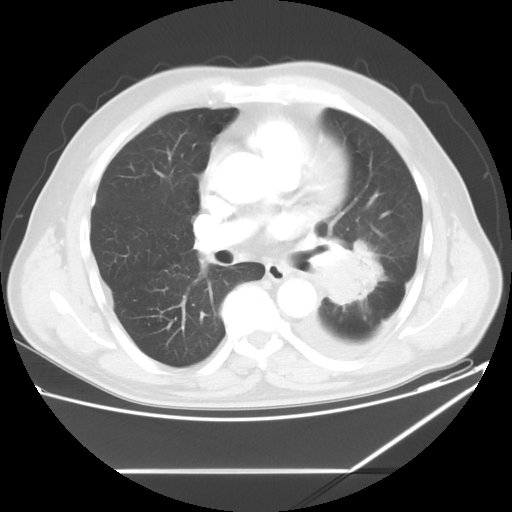
Chest CT, one axial slice. Slice 32 of 60 in the series (ordered by position). Reconstruction kernel STANDARD. 120 kVp. Lung window (W 1500 / L -600 HU). 5 mm slice thickness. 512 × 512 image matrix, field of view 395 × 395 mm. Male patient, age 62 years. Case-level facts recorded for this patient, not image findings: clinical TNM (as recorded): T3 N0 M1.
Structures marked on this image (bounding box drawn by a radiologist):
- lung tumour (recorded histology: adenocarcinoma): bounding box [x1, y1, x2, y2] px = [315, 242, 381, 313]
- lung tumour (recorded histology: adenocarcinoma): [318, 243, 379, 308]